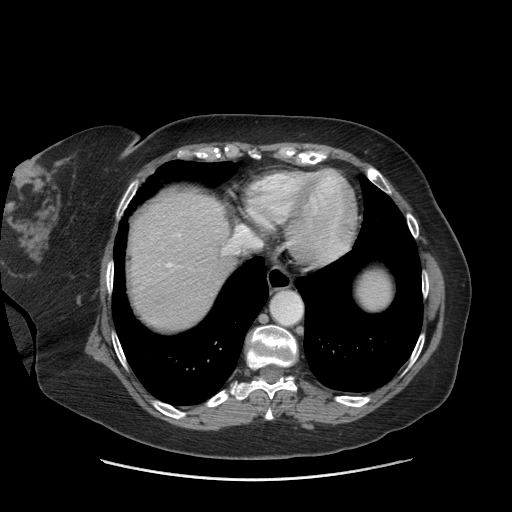
Contrast-enhanced abdominal CT (liver protocol), one axial slice; position 64 of 69 along the scan axis; reconstruction kernel STANDARD; 140 kVp; soft-tissue window (W 400 / L 40 HU); 2.5 mm slice thickness; 512 × 512 image matrix, field of view 420 × 420 mm. From the clinical record (not read from this slice): diagnosis: hepatocellular carcinoma (patient treated with transarterial chemoembolisation; whether this scan precedes or follows treatment is not stated here); TNM stage (as recorded): Stage-IIIB; Child-Pugh class: A; tumour differentiation: moderately differentiated.
Outlined on this slice (semi-automatically segmented with operator editing):
- abdominal aorta: bounding box <272,293,302,325> (left, top, right, bottom; pixels)
- liver parenchyma outside the tumour (the mass and vessels are separate outlines, so this box may not span the whole liver): <128,192,232,328>
- liver vessels: <166,234,180,267>